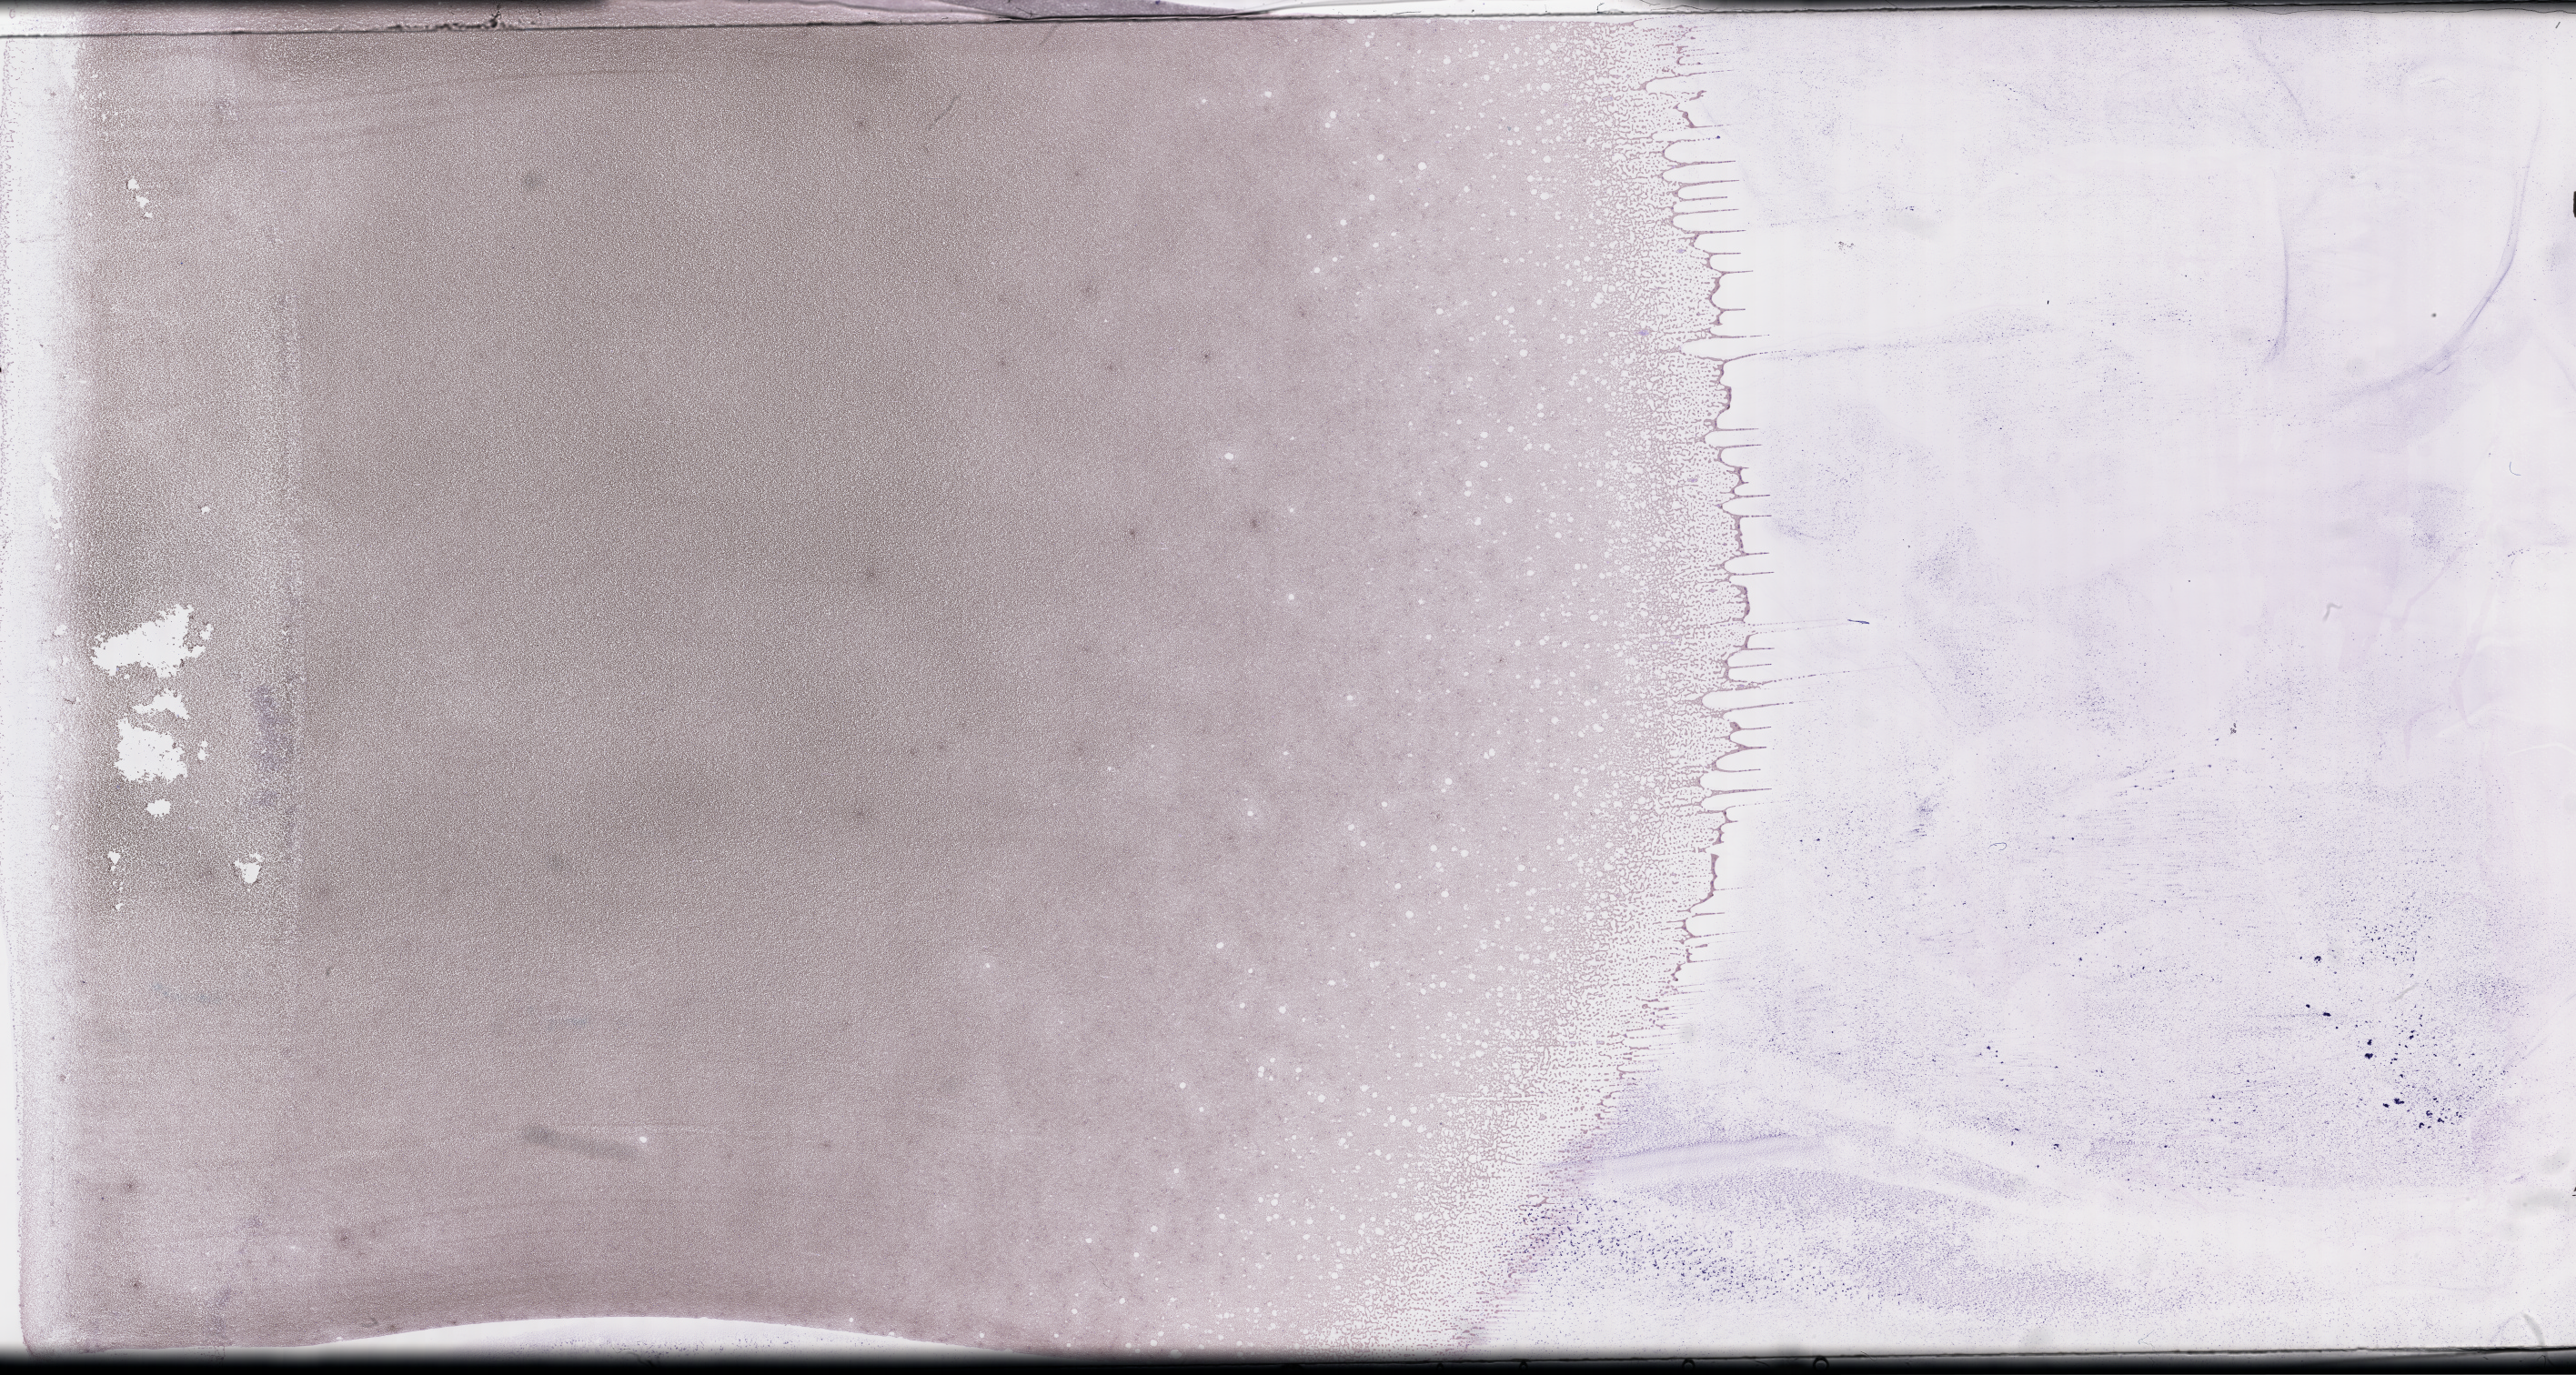
Whole-slide image of a whole blood smear, Wright–Giemsa stain — whole scanned area (about 45.7 x 24.4 mm) shown as a low-resolution overview. EDTA-anticoagulated smear. Male patient.
From a patient with: Plasma Cell Myeloma.